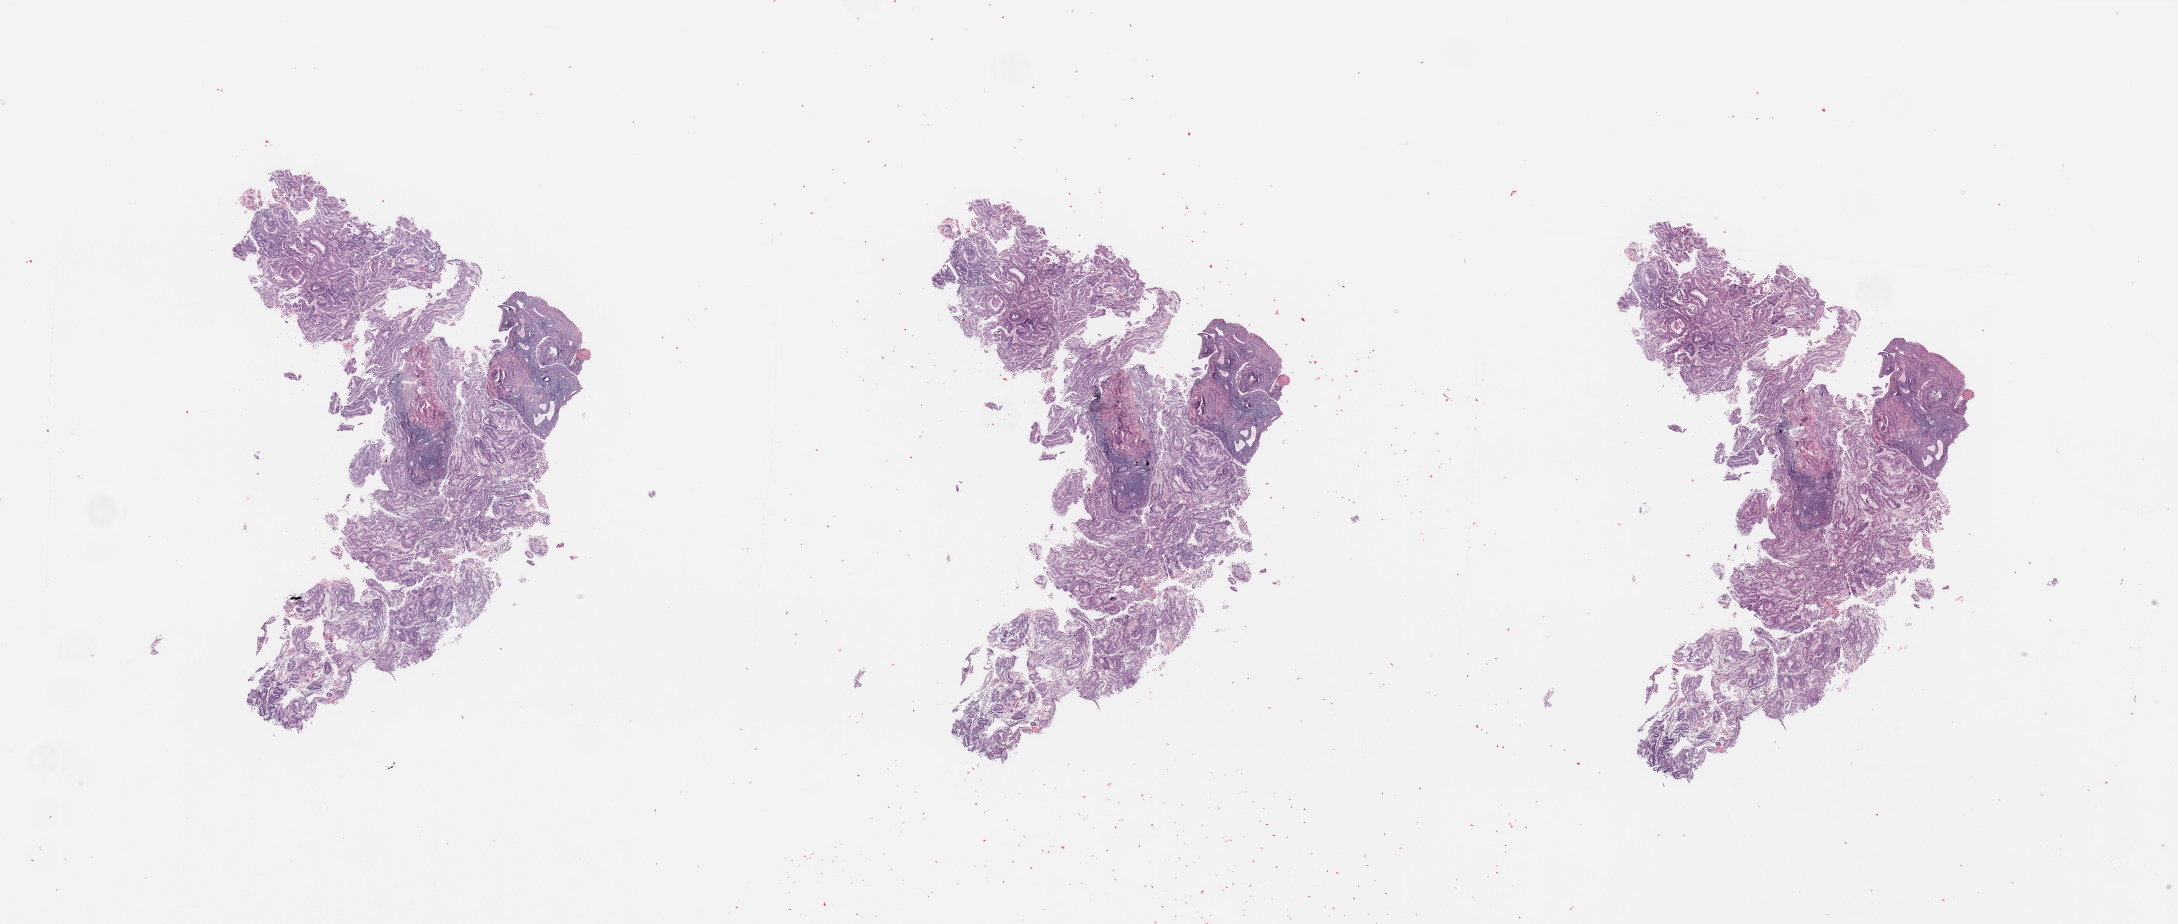
H&E-stained whole-slide image — low-resolution overview of the scanned area, about 34.5 x 14.6 mm. Tumour tissue sample, sampled site: uterus. Female, 77 y/o. Histologic grade: G1 (well differentiated). Pathologist review of this section (percent, as recorded): tumour nuclei 80%, necrosis 0%.
AJCC pathologic stage: I. Diagnosis: Endometrioid adenocarcinoma, NOS.